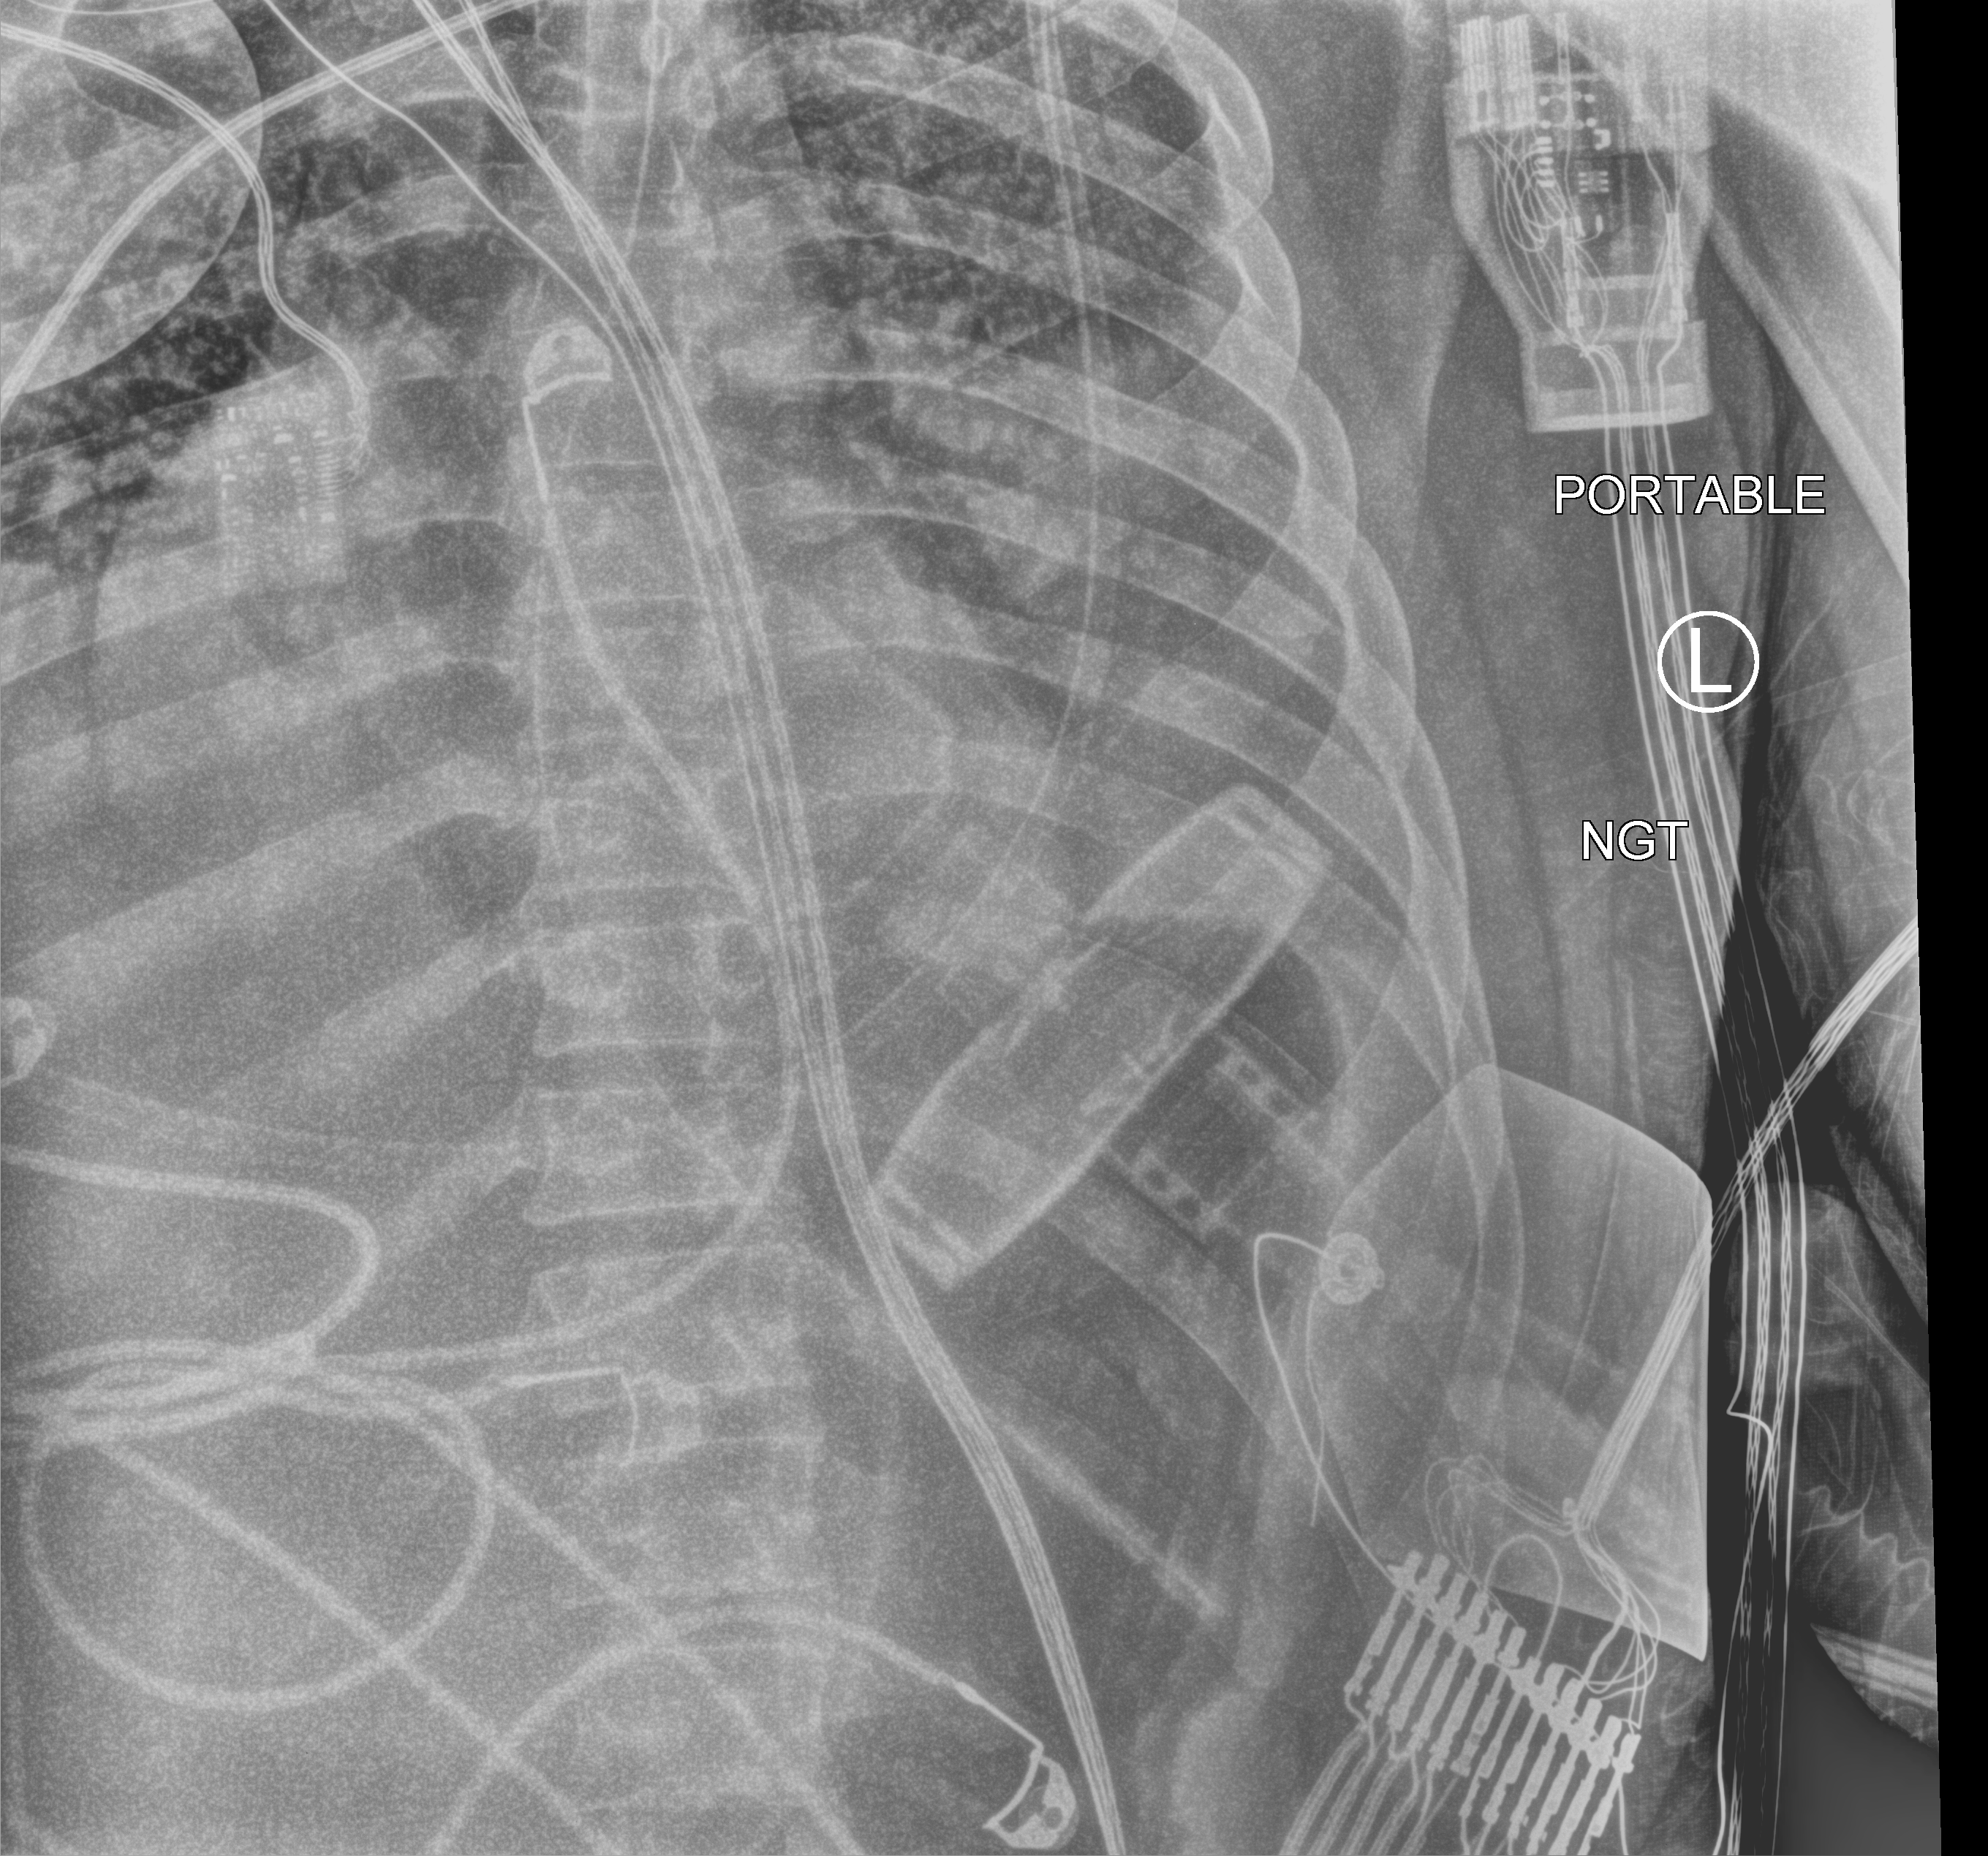
Abdomen X-ray (portable). Patient hospitalised with COVID-19; male, aged 18–59 years.
From the hospital-stay record, not from the radiograph (when in the stay this image was taken is not recorded):
- chronic kidney disease (admission record): no
- COPD (admission record): no